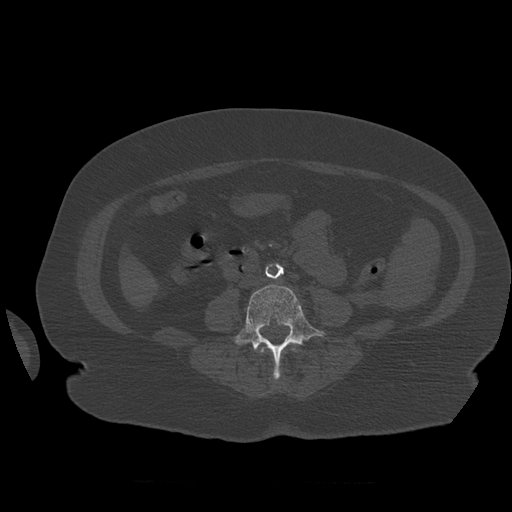
CT including the spine, one axial slice. Position 208 of 399 along the scan axis. Reconstruction kernel STANDARD. 120 kVp. Bone window (W 1800 / L 400 HU). 1.25 mm slice thickness. 512 × 512 image matrix, field of view 404 × 404 mm. Patient age 81 years. From the clinical record (not read from this slice): primary cancer: renal; vertebrae with lytic lesions (as recorded): L1.
Structures marked on this image (semi-automatically segmented with operator editing):
- L3 vertebra: bounding box (x1, y1, x2, y2) in pixels: (260, 347, 297, 354)
- L4 vertebra: (234, 284, 326, 380)